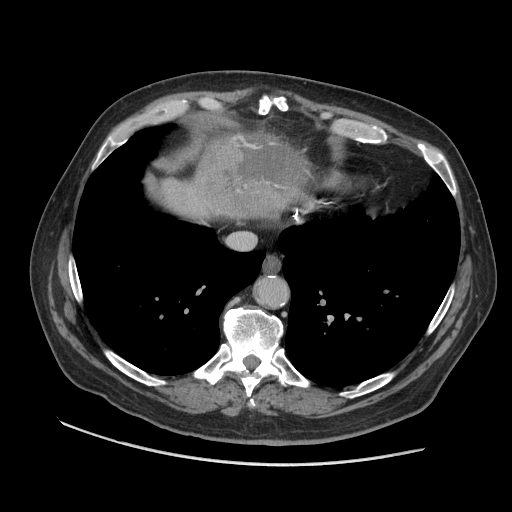
Contrast-enhanced abdominal CT (liver protocol), one axial slice. Position 93 of 109 along the scan axis. 140 kVp. Soft-tissue window (W 400 / L 40 HU). 2.5 mm slice thickness. 512 × 512 image matrix. From the clinical record (not read from this slice): diagnosis: hepatocellular carcinoma (patient treated with transarterial chemoembolisation; whether this scan precedes or follows treatment is not stated here); TNM stage (as recorded): Stage-I; Child-Pugh class: A; tumour nodularity: uninodular.
Annotated regions visible in this slice (semi-automatic segmentation, software-assisted and operator-edited):
- liver parenchyma outside the tumour (the mass and vessels are separate outlines, so this box may not span the whole liver): bounding box <148,134,302,218> (left, top, right, bottom; pixels)
- mass: <193,128,311,219>